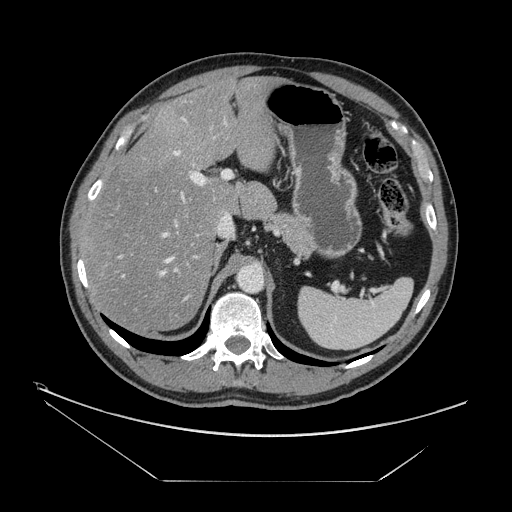
Contrast-enhanced abdominal CT, one axial slice; slice 97 of 161 in the series (ordered by position); reconstruction kernel STANDARD; intravenous contrast given; soft-tissue window (W 400 / L 40 HU); 2.5 mm slice thickness; 512 × 512 image matrix, field of view 440 × 440 mm. Male patient, age 65 years. Case-level facts recorded for this patient, not image findings: diagnosis: colorectal cancer liver metastases, imaged before liver resection; multiple liver metastases: yes; largest metastasis: 4.2 cm; disease in both lobes: yes.
Outlined on this slice (manually delineated by an expert):
- hepatic veins: bounding box [x1, y1, x2, y2] px = [122, 118, 185, 278]
- liver: [84, 78, 275, 330]
- planned liver remnant (the part of the liver to remain after resection): [84, 78, 275, 330]
- portal vein (with intrahepatic branches): [117, 150, 231, 316]